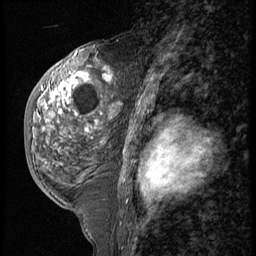
Breast MRI (dynamic contrast-enhanced), one sagittal slice. 3 images stored at this slice position (order not interpretable as contrast timing). 1.5 T. TE 4.2 ms, TR 9 ms. 2.5 mm slice thickness. 256 × 256 image matrix, field of view 180 × 180 mm. Patient: female, 50 years. From the clinical record (not read from this slice): setting: breast cancer imaged before/during neoadjuvant chemotherapy; receptor status: triple-negative.
Structures marked on this image (semi-automatic segmentation, software-assisted and operator-edited):
- analysis volume of interest (the breast-tissue region the enhancement analysis was run in; not a lesion): bounding box [x1, y1, x2, y2] px = [25, 50, 119, 191]
- tumour enhancement mask (voxels above the 140 % enhancement threshold inside the analysis volume of interest): [42, 67, 113, 133]